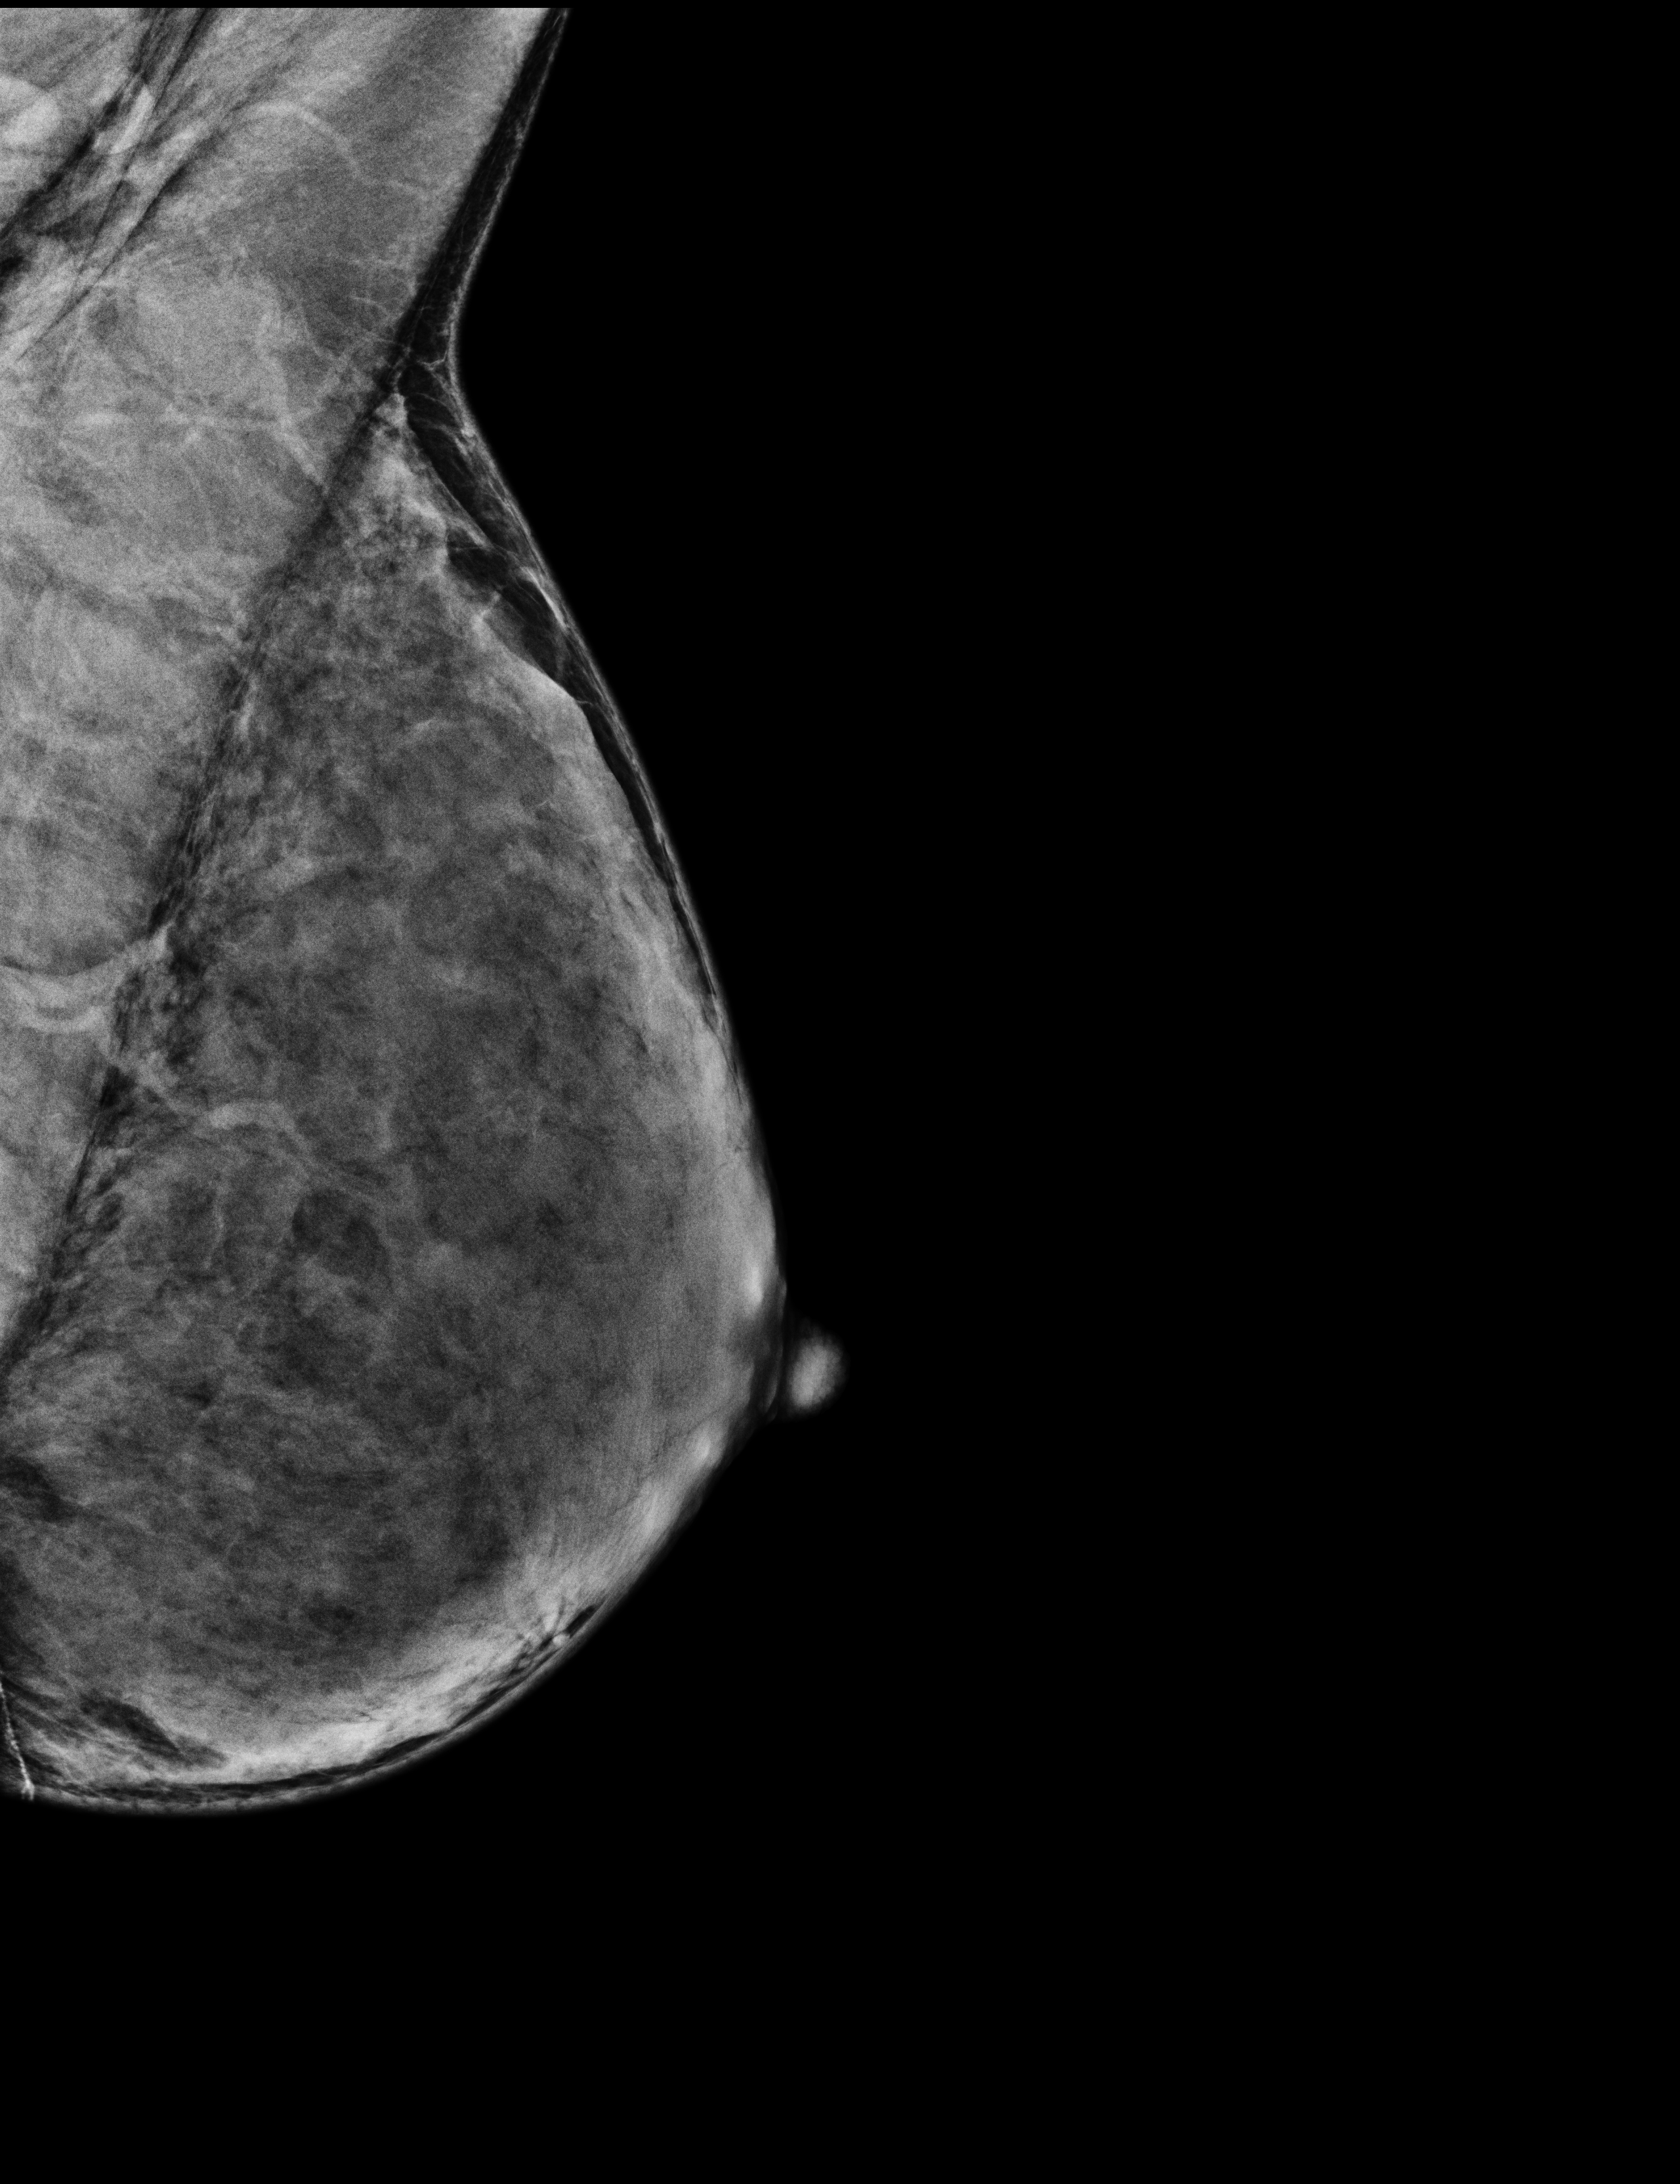
Digital mammogram (FFDM); left breast; medio-lateral oblique projection; annual screening mammography examination; compressed breast thickness 34 mm; system: Selenia Dimensions. Patient aged 54 years (female).
- breast density at the screening exam (both breasts): extremely dense (BI-RADS density category d)
- final BI-RADS category for the screening round (tomosynthesis exam, both breasts): category 1
- recall: no recall after this screen